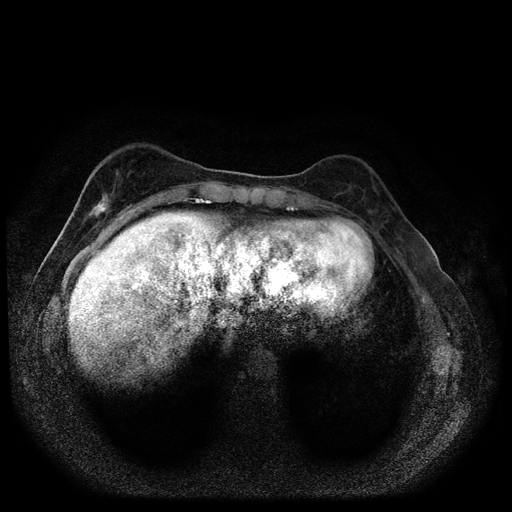
Breast MRI (dynamic contrast-enhanced, multi-phase), one axial slice. Position 28 of 116 along the scan axis. Dynamic contrast-enhanced series, time point 2 of 5 at this slice position (early post-contrast). 1.5 T. TE 2.7 ms, TR 5.4 ms. 512 × 512 image matrix, field of view 330 × 330 mm. Female patient, age 49 years.
Structures marked on this image (semi-automatic segmentation, software-assisted and operator-edited):
- breast lesion (labelled 'tumour' in the annotation; benign lesions carry a separate 'benign' label): box from (x=87, y=169) to (x=123, y=219) px